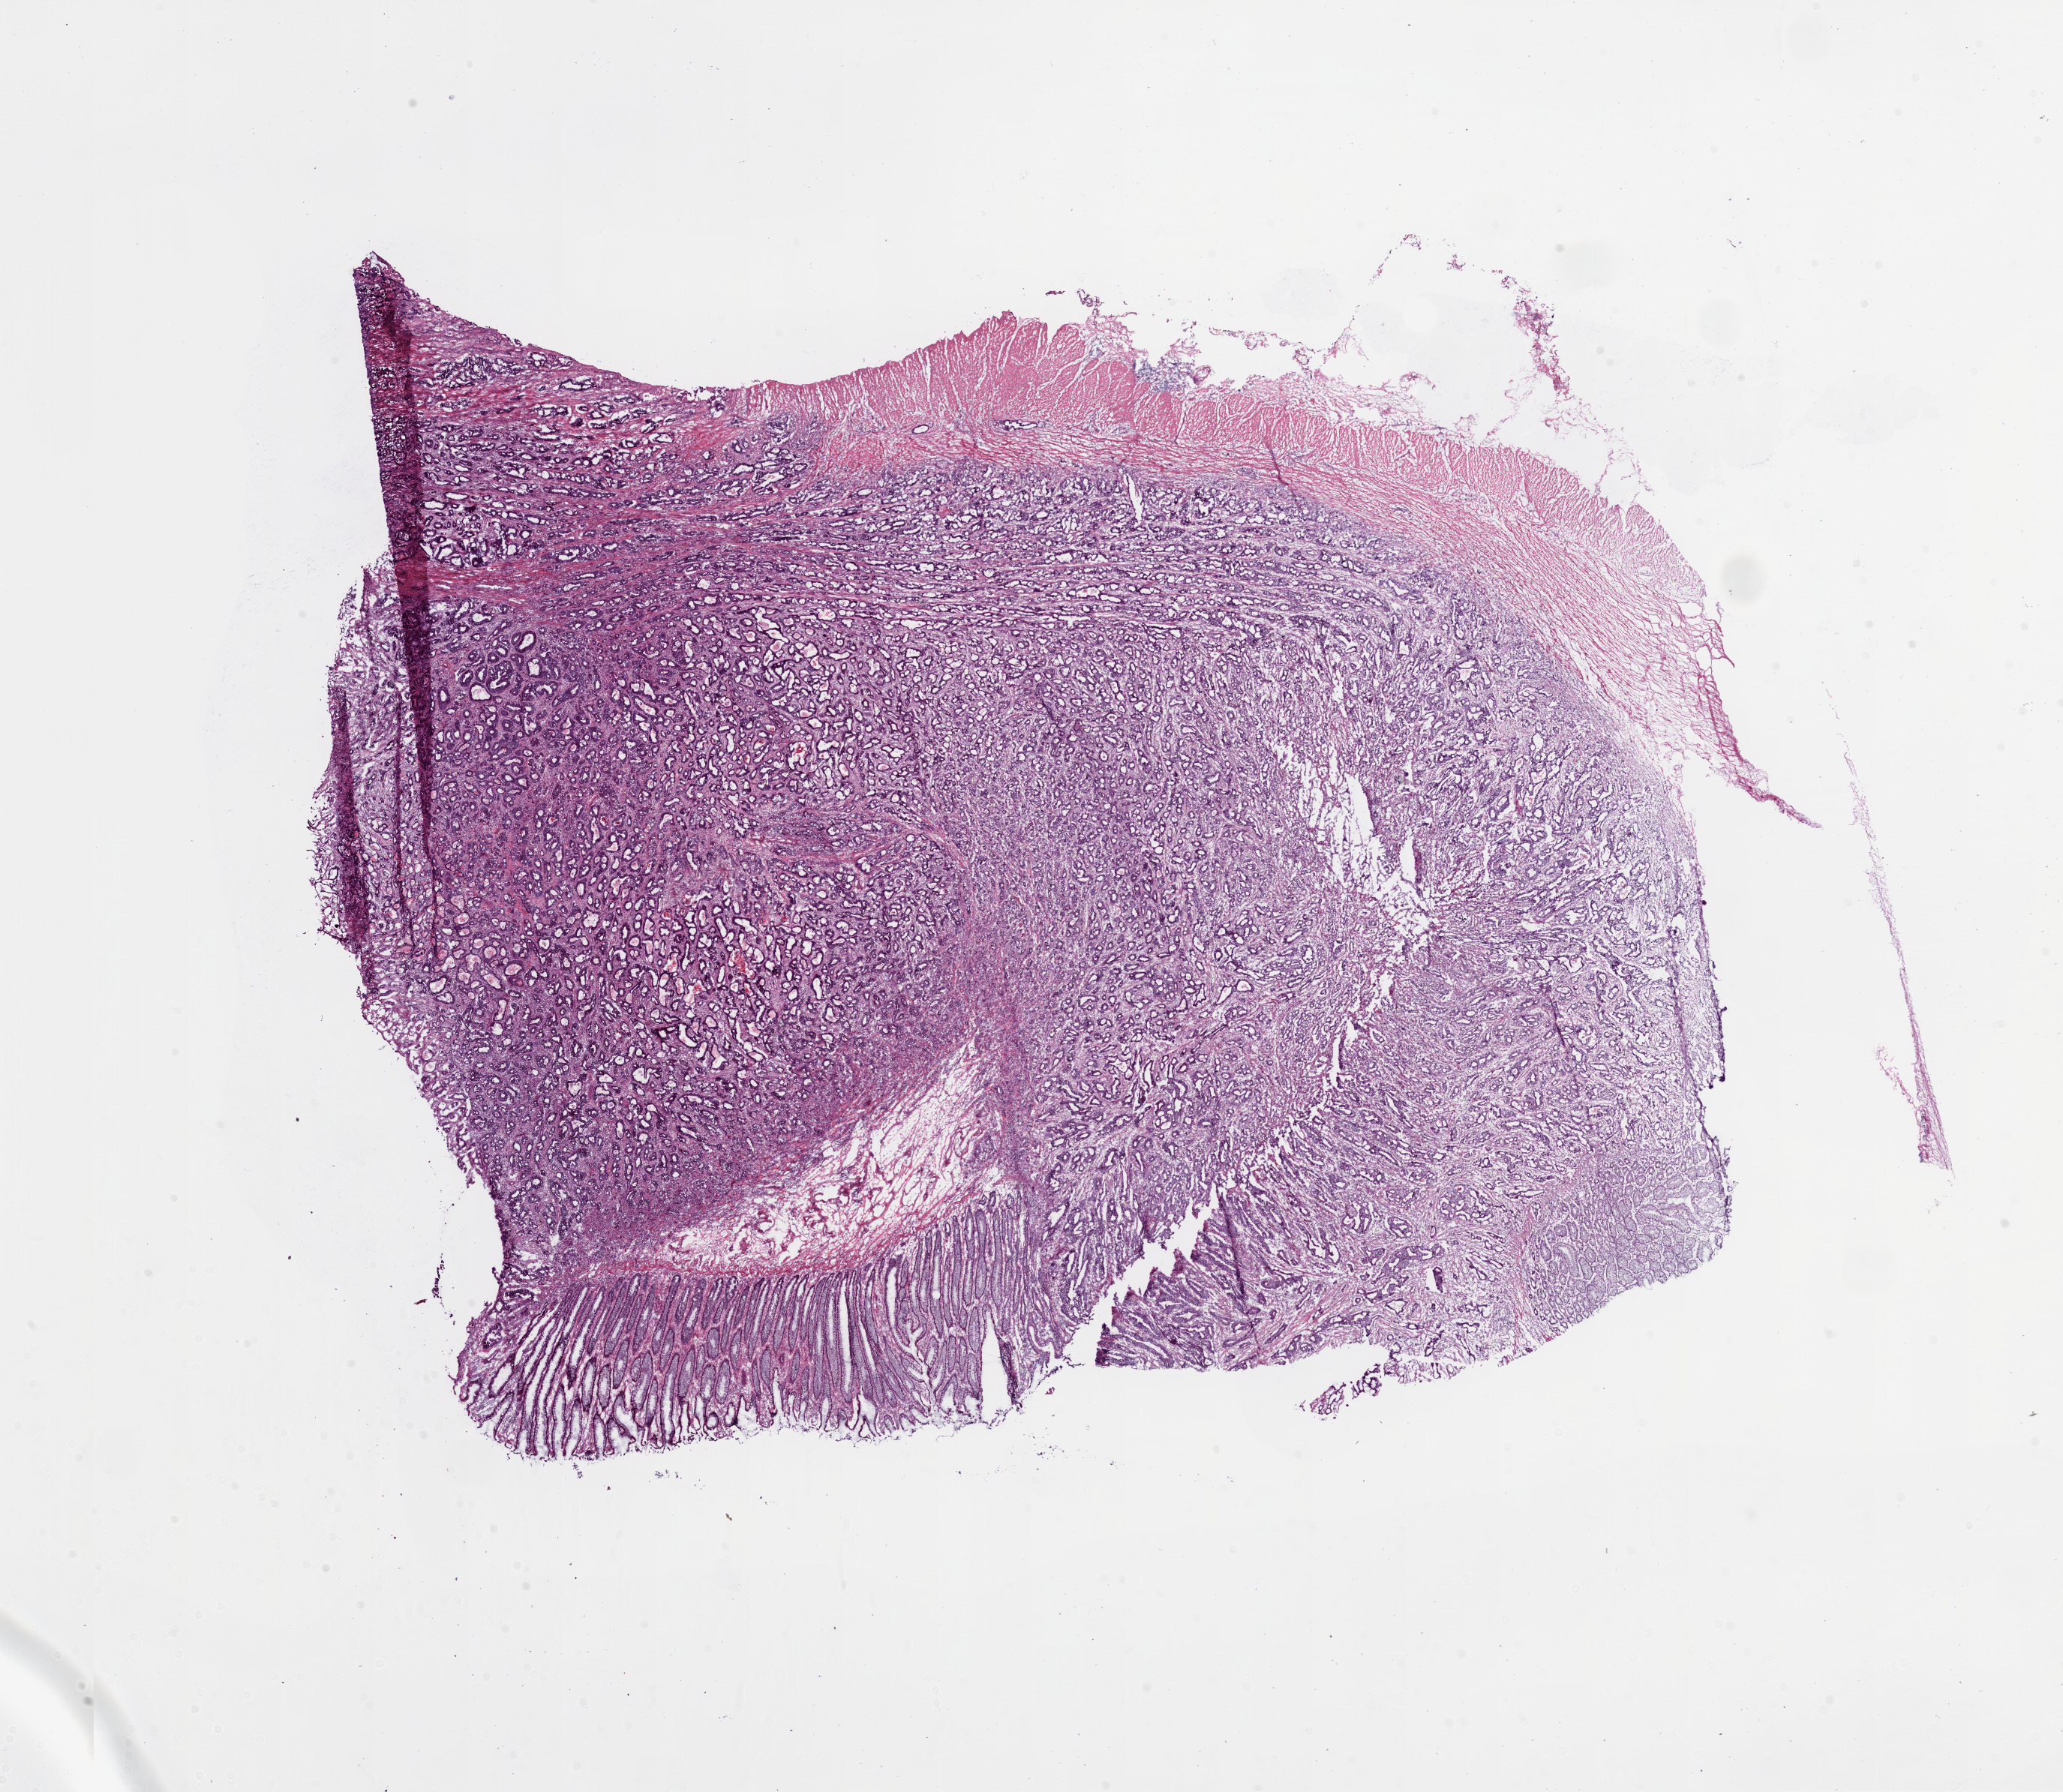
Digitized H&E tissue section (whole slide), low-resolution overview of the scanned area, about 22.1 x 19.2 mm. Frozen section. Primary tumour sample from the colon. Female patient; age at initial diagnosis 47 years. Composition of this section per pathologist review: tumour cells 76%, tumour nuclei 76%, normal cells 20%, stromal cells 6%, necrosis 0%. Inflammatory infiltration, as recorded: lymphocyte infiltration 5%.
AJCC pathologic stage: IIIB (6th edition). Lymph nodes positive (case pathology): 3 of 14 examined. Pathologic diagnosis: Adenocarcinoma, NOS.